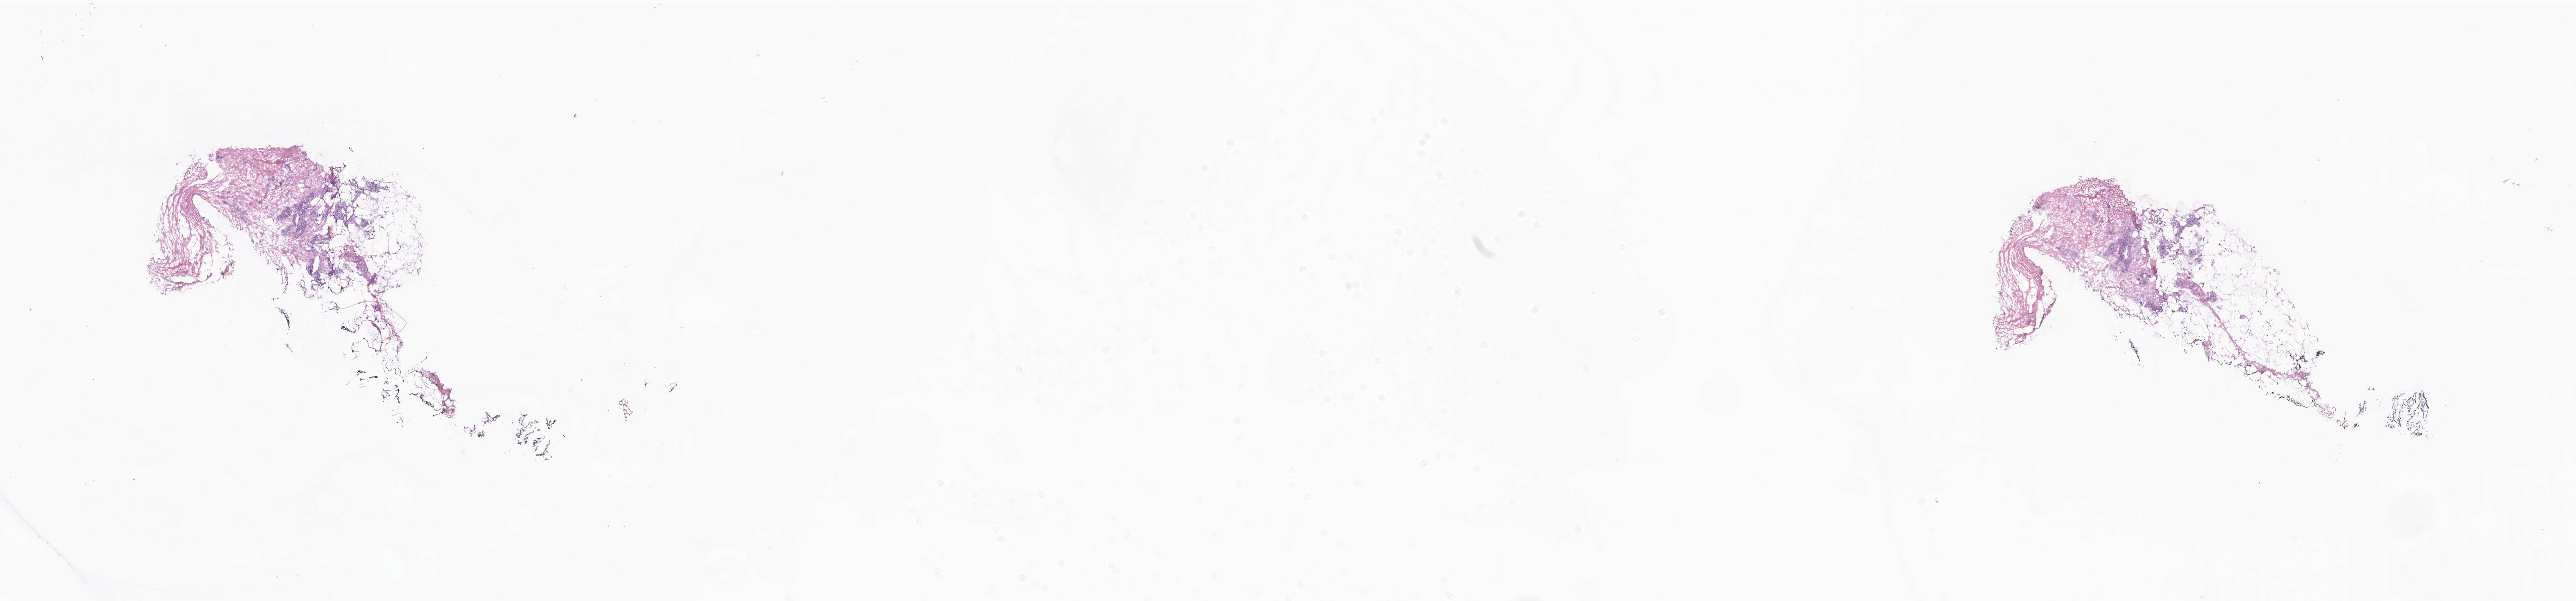
Digitized hematoxylin and eosin (H&E)-stained section — whole scanned area (about 33.4 x 7.8 mm) shown as a low-resolution overview. Frozen section (tissue freezing medium). Specimen: primary tumor. Anatomic site: breast. Female patient; age at initial diagnosis 67 years.
Diagnosis: Infiltrating duct carcinoma, NOS.